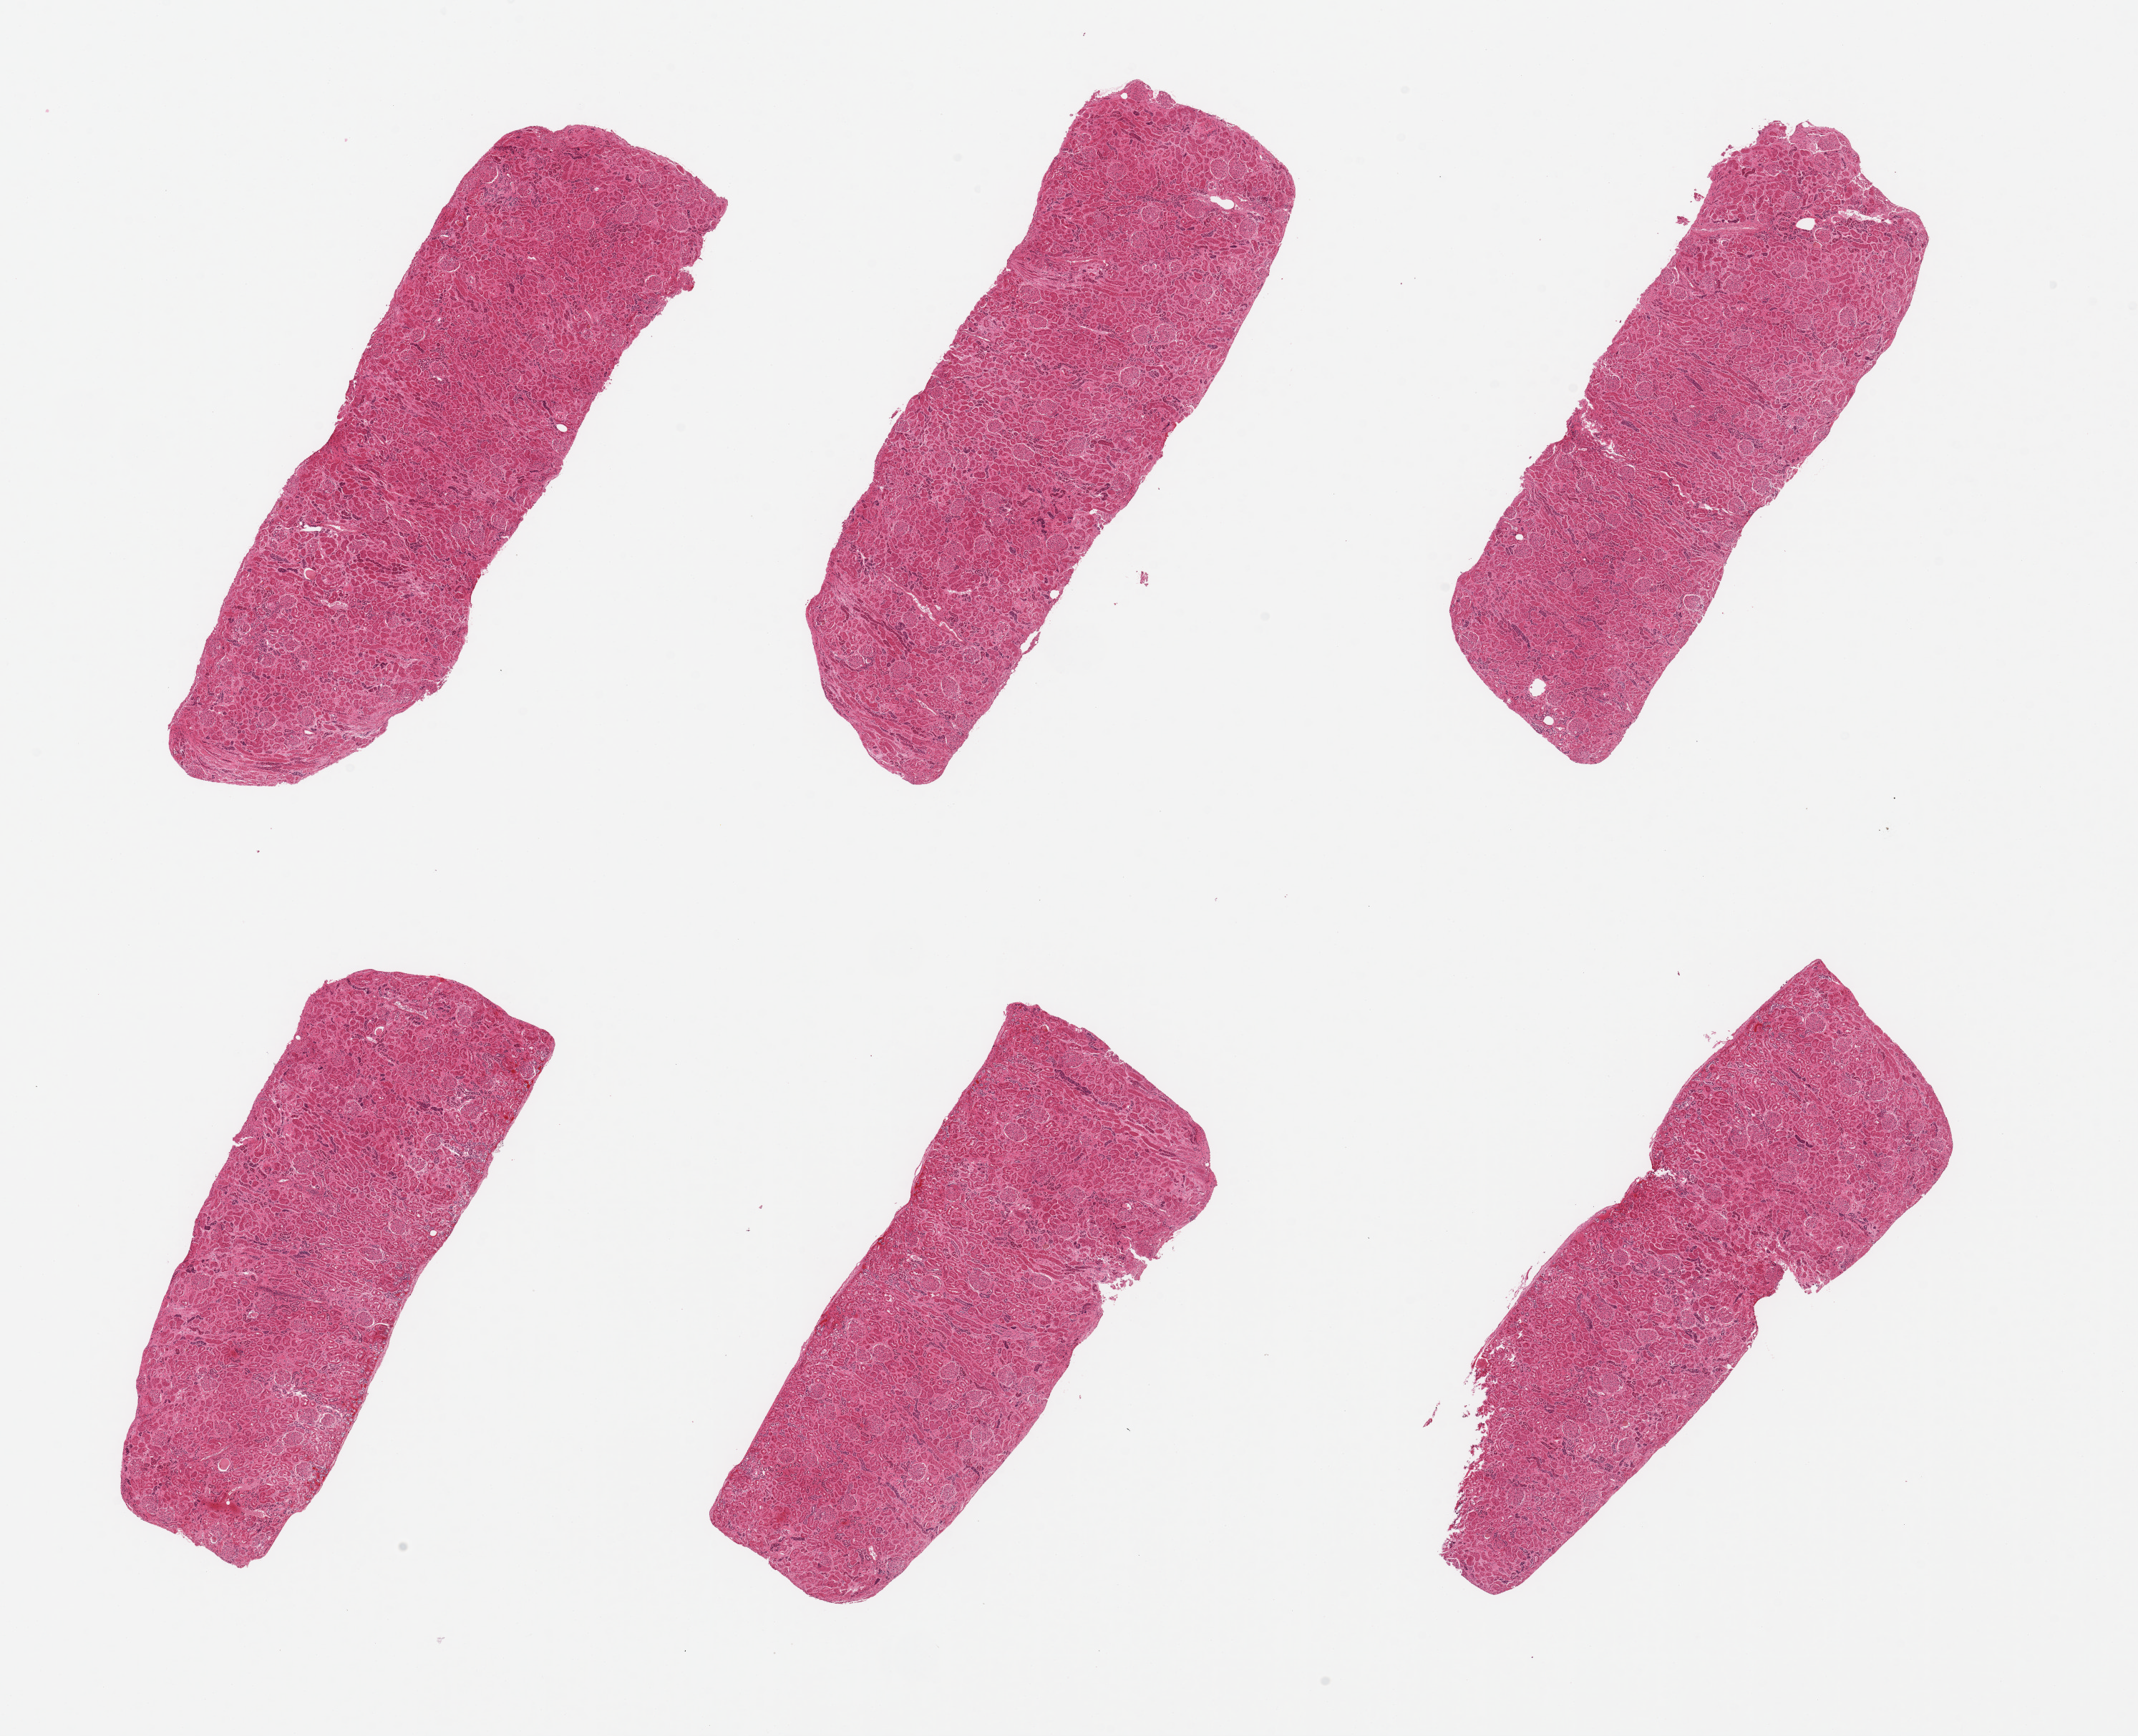
H&E whole-slide image, brightfield — low-resolution overview of the scanned area, about 23.6 x 19.2 mm (acquisition: 20x scan). PAXgene-fixed paraffin-embedded (PFPE) section. Target tissue: renal cortex. Tissue donor sample. Donor: female.
Reviewer comment on this tissue sample: 6 pieces, glomeruli present, tubules autolyzed.